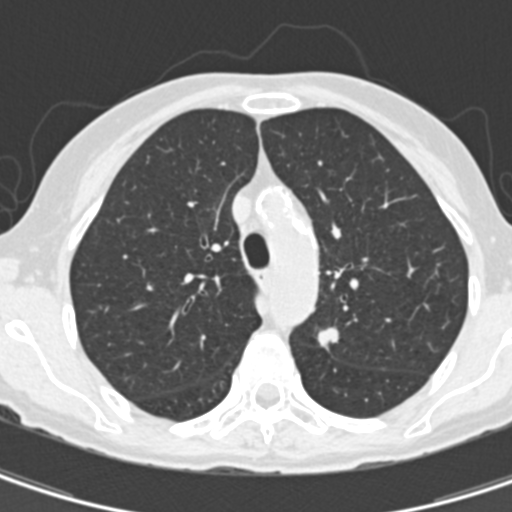
Chest CT (low-dose screening protocol), one axial image. Baseline screening round. Lung window (W 1500 / L -600 HU). 2 mm slice thickness. Standard (soft-tissue) reconstruction kernel (B30f). 120 kVp. 512 × 512 image matrix. Female participant, aged 67 years at enrolment. Current smoker at enrolment.
Expert-annotated lung lesion, bounding box (x1, y1, x2, y2) in pixels: (311, 318, 353, 368). Reader record for this screening exam (exam-level; its link to the box is not recorded): non-calcified nodule or mass ≥4 mm, left upper lobe, 11 × 8 mm, spiculated (stellate) margins, soft tissue attenuation. Participant outcome: lung cancer diagnosed 73 days after this screen — adenocarcinoma, NOS, left upper lobe, poorly differentiated (G3), stage IA (AJCC 6th edition), 13 mm at pathology.